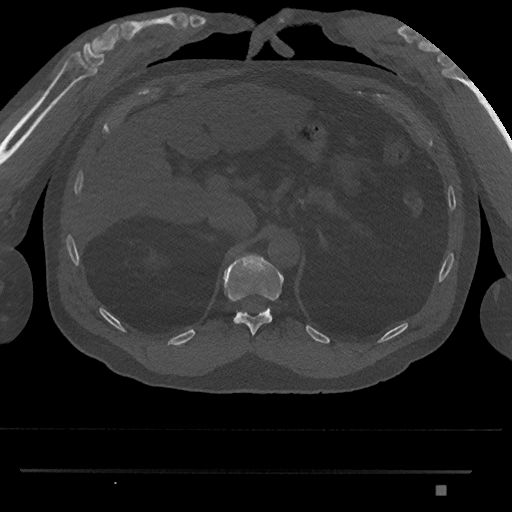
CT including the spine, one axial slice; slice 937 of 1134 in the series (ordered by position); 120 kVp; bone window (W 1800 / L 400 HU); 0.5 mm slice thickness; 512 × 512 image matrix, field of view 429 × 429 mm. Patient: male, 65 years. Case-level facts recorded for this patient, not image findings: primary cancer: prostate.
Outlined on this slice (semi-automatically segmented with operator editing):
- T11 vertebra: bounding box (x1, y1, x2, y2) in pixels: (223, 254, 284, 336)